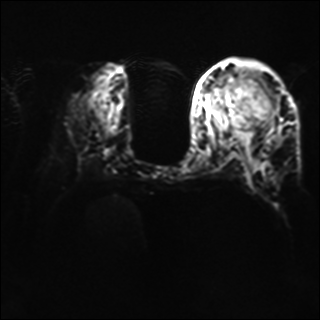
Breast MRI, one axial slice; position 19 of 40 along the scan axis; diffusion-weighted series; image 2 of 4 stored at this slice position (different b-values; order by instance number); 1.5 T; 320 × 320 image matrix, field of view 320 × 320 mm. Female patient.
Annotated regions visible in this slice (manually delineated by an expert):
- tumour on diffusion-weighted imaging: bounding box (x1, y1, x2, y2) in pixels: (223, 81, 241, 114)